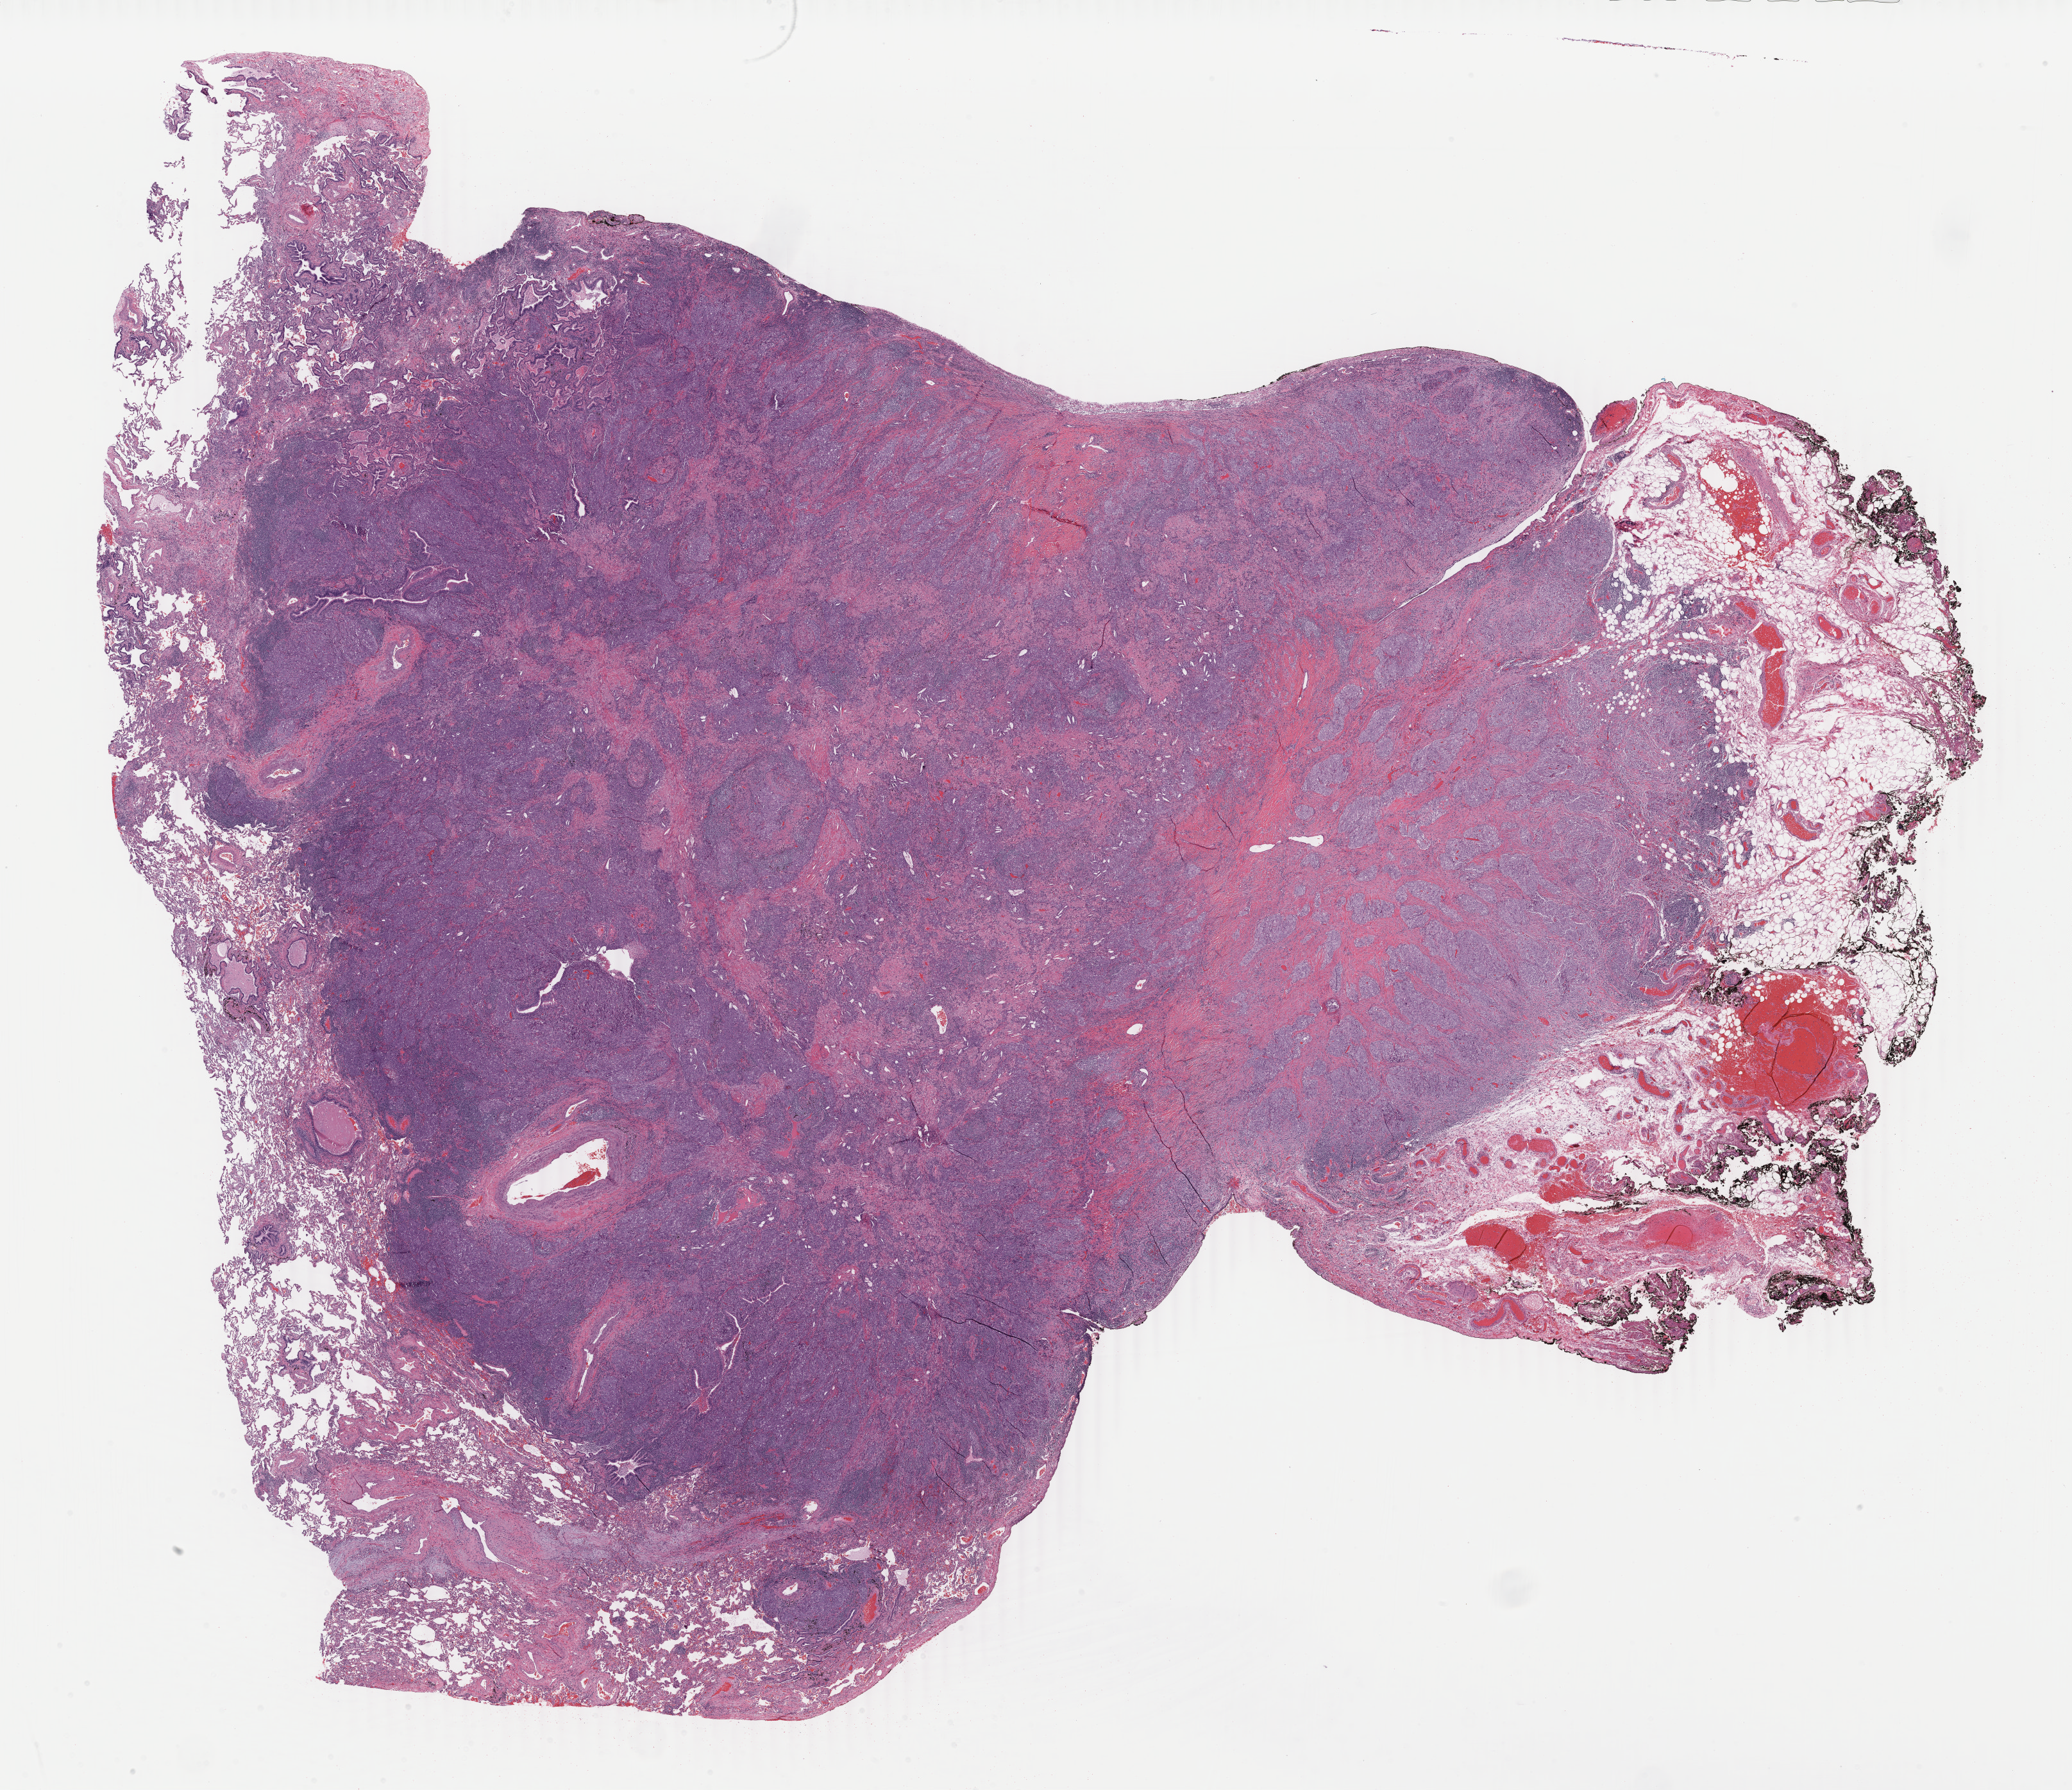
H&E whole-slide image, shown as a low-resolution overview of the whole scanned area (about 25.7 x 22.2 mm); formalin-fixed paraffin-embedded (FFPE) diagnostic section; sample: primary tumour, lung. Patient: female, age at initial diagnosis 78 years.
Pathologic diagnosis: Squamous cell carcinoma, NOS (lower lobe, lung). TNM: T2a N1 M0. AJCC pathologic stage: IIA. Laterality: left.